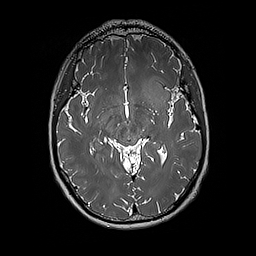
Brain MRI from a brain-tumour surgery series, one axial slice; slice 107 of 192 in the series (ordered by position); 256 × 256 image matrix, field of view 250 × 250 mm. Case-level facts recorded for this patient, not image findings: histopathology: Glioblastoma; WHO grade: 4; IDH mutation: no; tumour location: Left Insular.
Outlined on this slice (manually delineated by an expert):
- tumour: bounding box <142,76,171,109> (left, top, right, bottom; pixels)